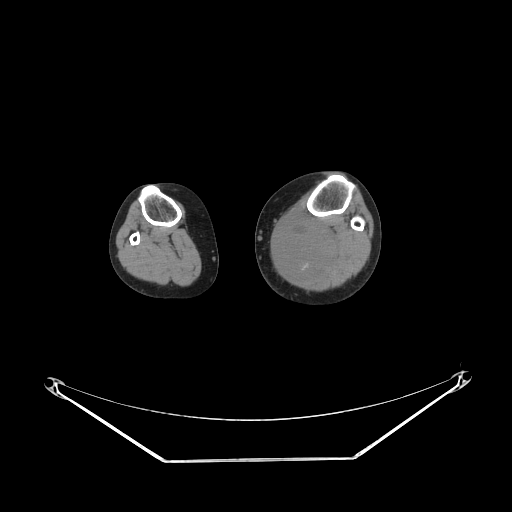
CT of an extremity soft-tissue mass (from a PET/CT study), one axial slice. Slice 153 of 223 in the series (ordered by position). Soft-tissue window (W 400 / L 40 HU). 3.75 mm slice thickness. 512 × 512 image matrix, field of view 500 × 500 mm. Female patient. Case-level facts recorded for this patient, not image findings: histological type: extraskeletal high grade osteogenic sarcoma; grade: high; site of the primary tumour: left calf.
Structures marked on this image (expert contour drawn on MRI and transferred to this co-registered scan by the dataset authors):
- gross tumour volume (mass): box from (x=274, y=217) to (x=339, y=277) px